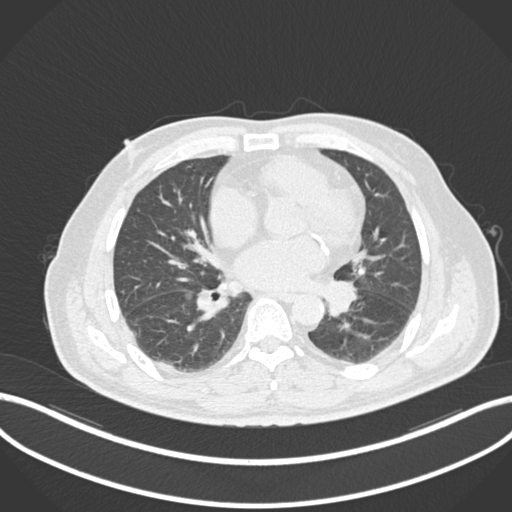
Chest CT, one axial slice. Slice 60 of 161 in the series (ordered by position). 120 kVp. Lung window (W 1500 / L -600 HU). 1 mm slice thickness. 512 × 512 image matrix, field of view 400 × 400 mm. Male patient, age 71 years. From the clinical record (not read from this slice): clinical TNM (as recorded): T1b N0 M0.
Outlined on this slice (rectangle marked by the reading radiologist):
- lung tumour (recorded histology: squamous cell carcinoma): bounding box <325,279,359,323> (left, top, right, bottom; pixels)